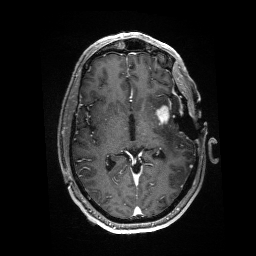
Brain MRI from a brain-tumour surgery series, one axial slice. Slice 88 of 176 in the series (ordered by position). T1-weighted post-contrast. 1 mm slice thickness. 256 × 256 image matrix, field of view 256 × 256 mm. Case-level facts recorded for this patient, not image findings: histopathology: Glioblastoma; WHO grade: 4; IDH mutation: no; tumour location: Left Anterior/Superior Temporal.
Structures marked on this image (expert manual segmentation):
- residual tumour: bounding box <155,105,170,124> (left, top, right, bottom; pixels)